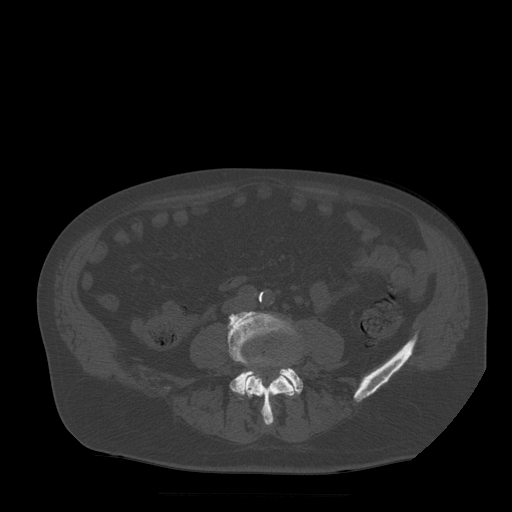
CT including the spine, one axial slice; slice 105 of 522 in the series (ordered by position); bone window (W 1800 / L 400 HU); 512 × 512 image matrix, field of view 420 × 420 mm. Patient age 72 years. From the clinical record (not read from this slice): primary cancer: prostate.
Structures marked on this image (semi-automatically segmented with operator editing):
- L4 vertebra: bounding box <228,312,296,427> (left, top, right, bottom; pixels)
- L5 vertebra: <230,355,303,400>